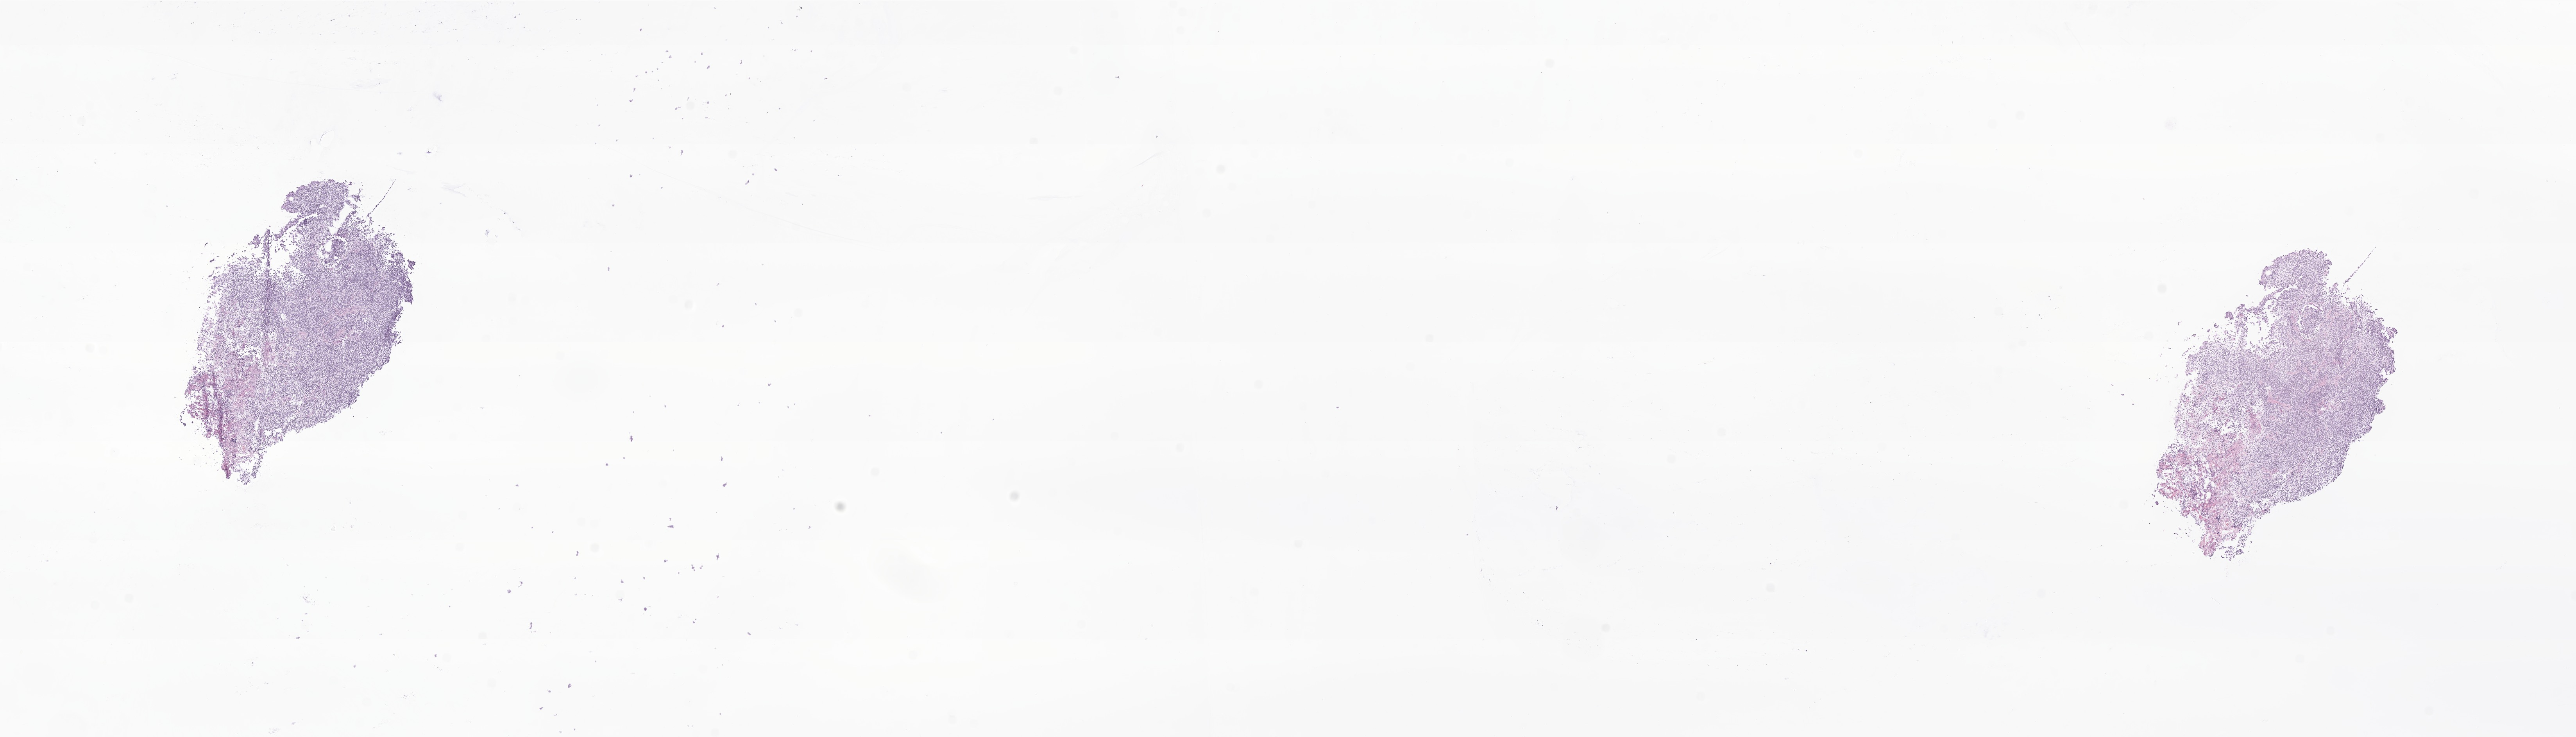
Whole-slide image, haematoxylin and eosin stain of tumor tissue from the cerebellum, shown as a low-resolution overview of the whole scanned area (about 27.8 x 7.9 mm). Frozen section (OCT-embedded). Patient male; age 75 months (6 years 3 months).
Diagnosis (ICD-O-3 morphology term): Medulloblastoma, NOS.